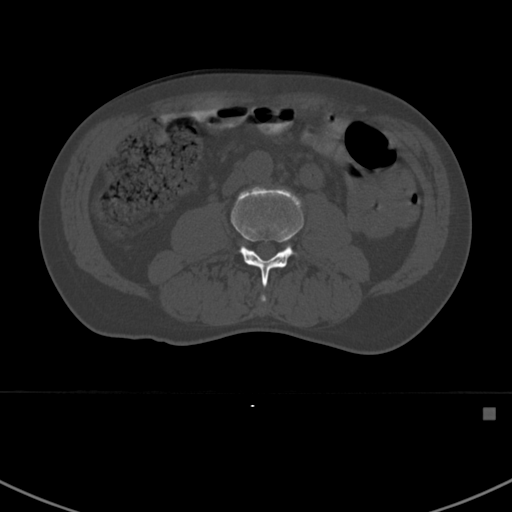
CT including the spine, one axial slice; slice 262 of 412 in the series (ordered by position); 120 kVp; bone window (W 1800 / L 400 HU); 1.5 mm slice thickness; 512 × 512 image matrix, field of view 358 × 358 mm. Male patient, age 59 years. From the clinical record (not read from this slice): primary cancer: prostate.
Structures marked on this image (semi-automatic segmentation, software-assisted and operator-edited):
- L3 vertebra: box from (x=230, y=186) to (x=305, y=303) px